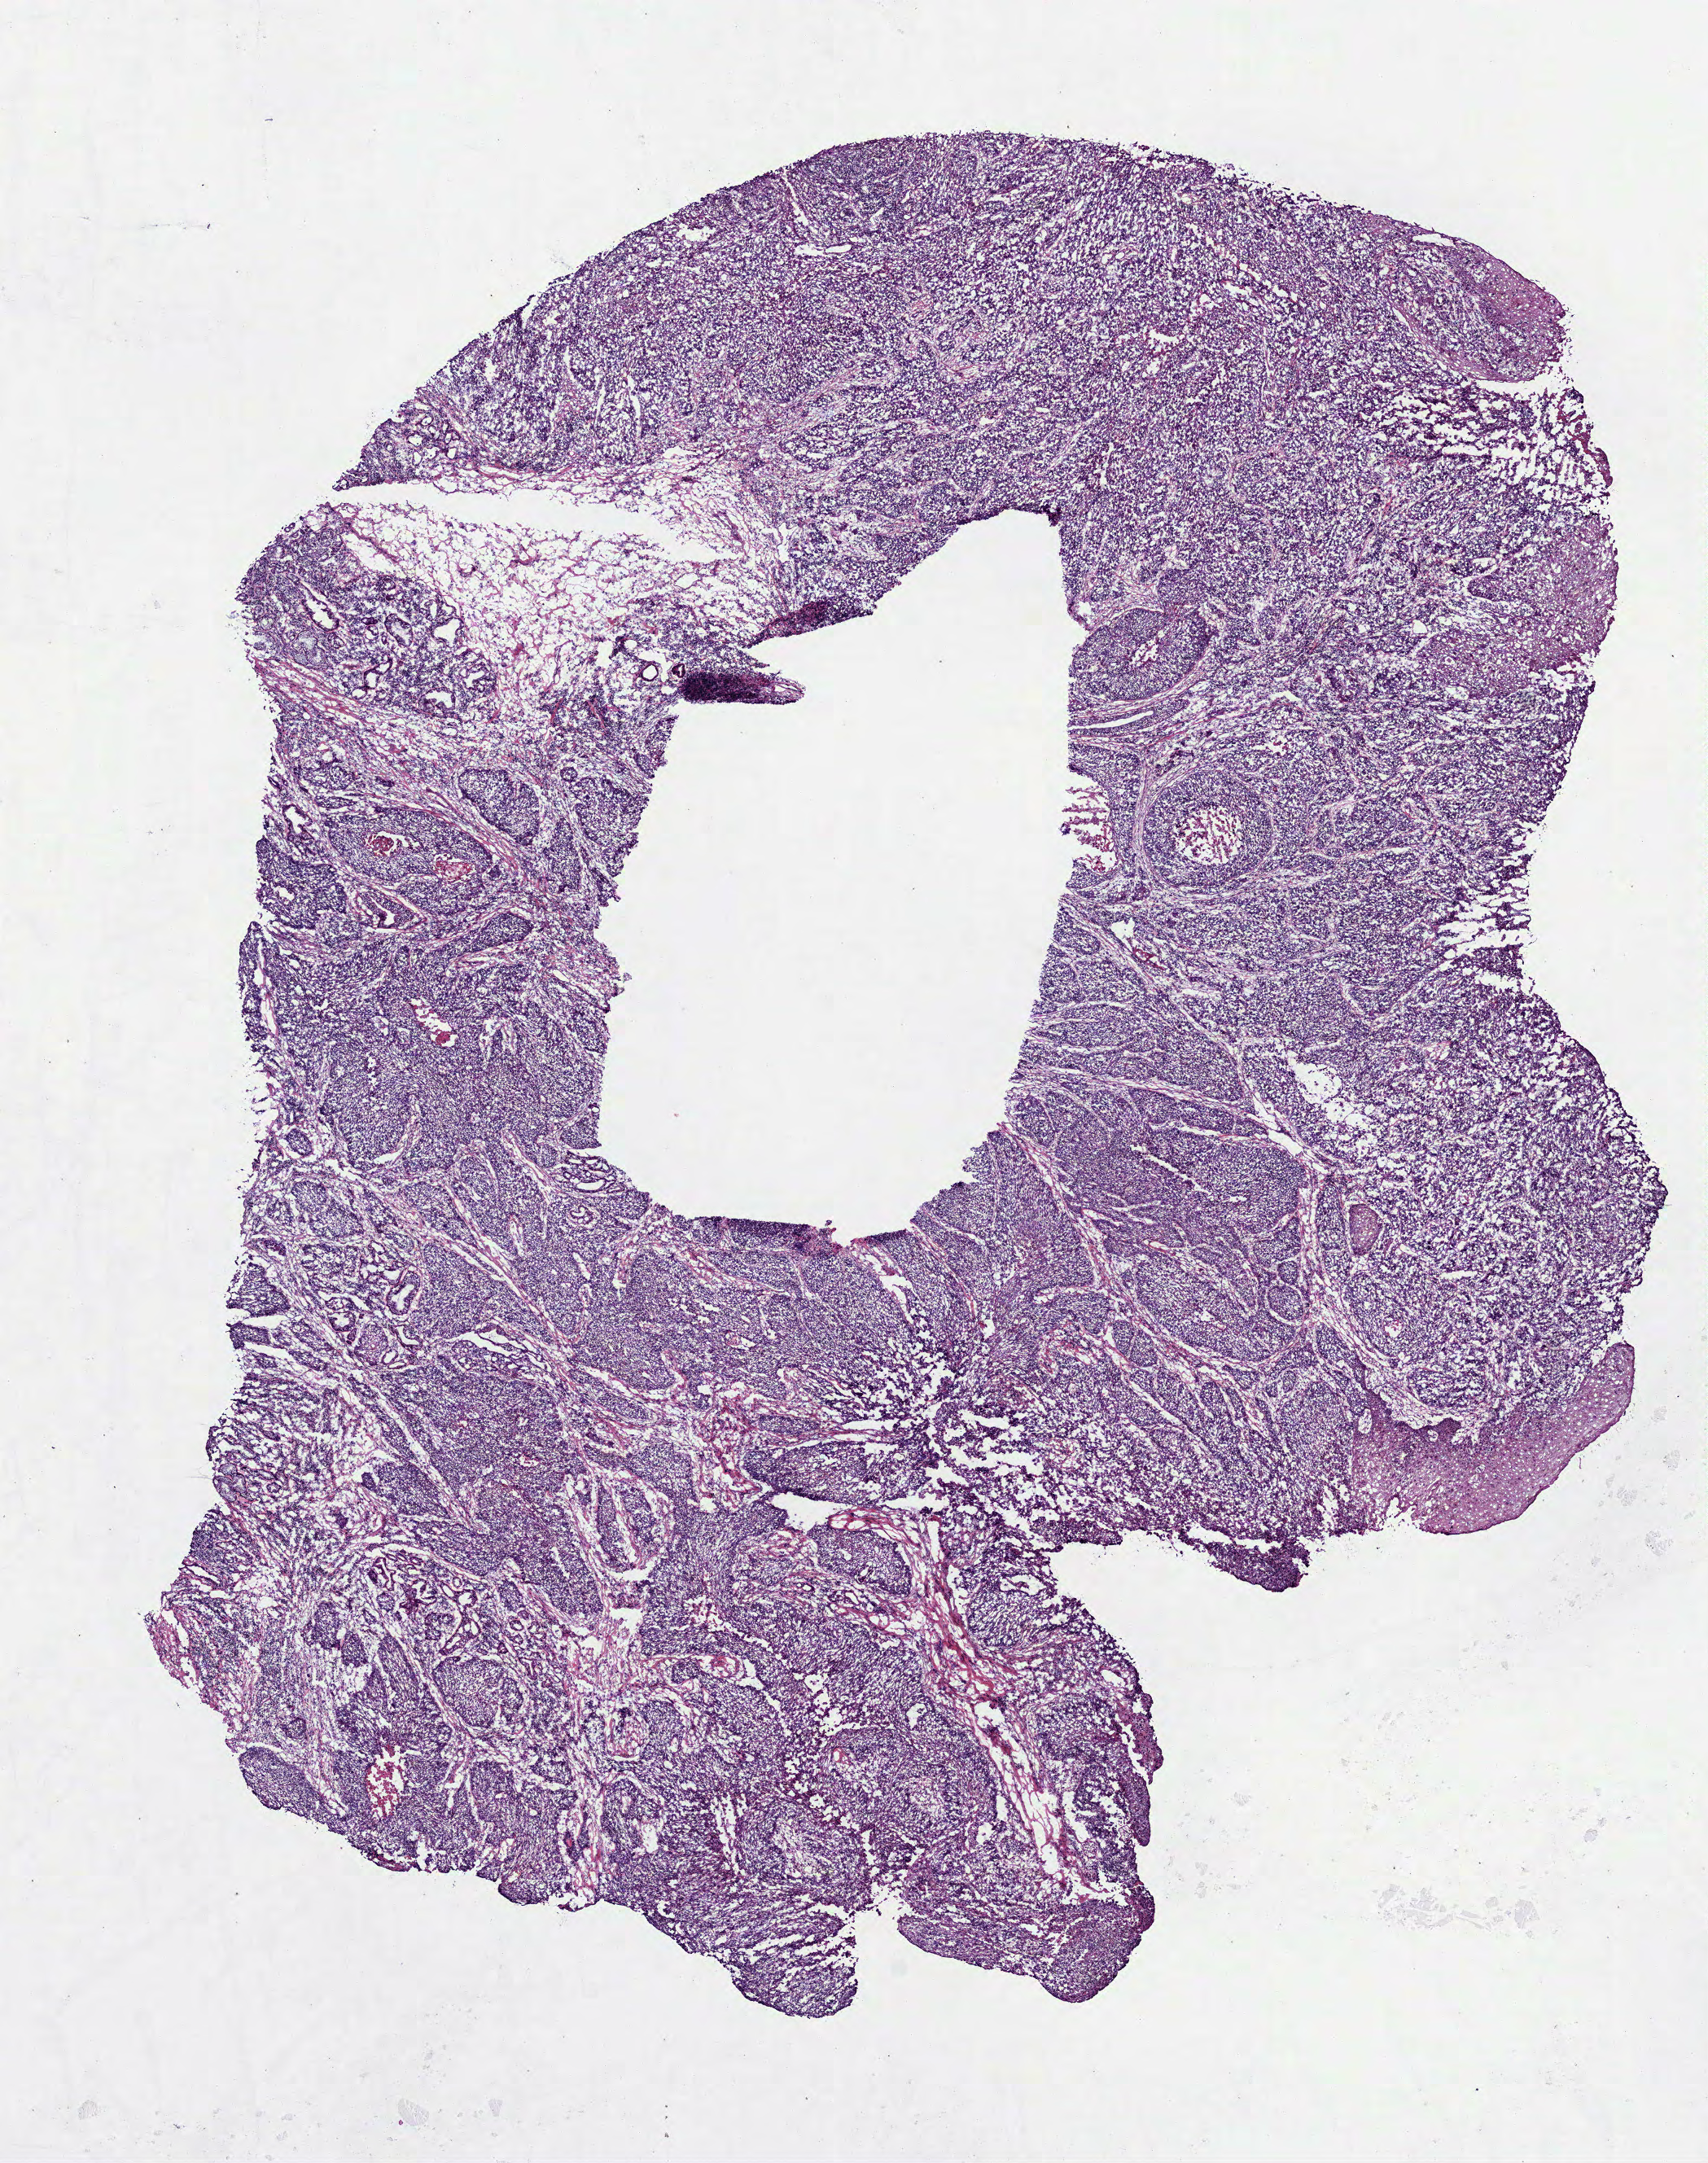
Whole-slide histology image, H&E-stained — a low-resolution overview of the entire scanned area, about 8.5 x 10.7 mm, frozen section from the bottom of the tissue portion, primary tumour sample from the head and neck. Male, age 53 years at initial diagnosis. Histologic grade: G2 (moderately differentiated). Pathologist review of this section (percent, as recorded): tumour cells 85%, tumour nuclei 85%, normal cells 0%, stromal cells 10%, necrosis 5%.
- AJCC pathologic stage: IVA
- histologic diagnosis: Squamous cell carcinoma, NOS (larynx, NOS)